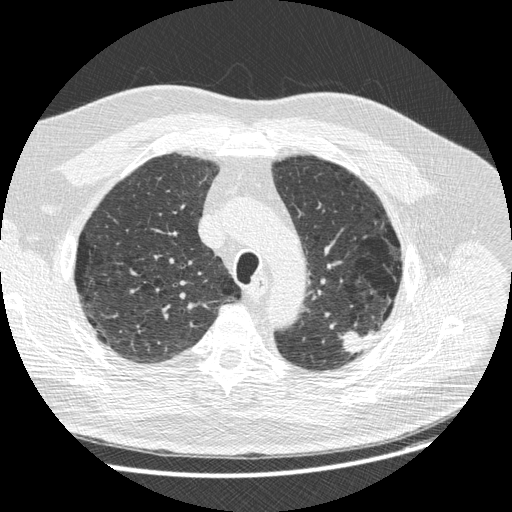
Low-dose screening chest CT, one axial slice; slice 202 of 258 in the series (ordered by position); reconstruction kernel STANDARD; lung window (W 1500 / L -600 HU); 512 × 512 image matrix.
Annotated regions visible in this slice (manually delineated by an expert):
- lesion 1 (tumor, upper lobe of left lung): bounding box [x1, y1, x2, y2] px = [341, 331, 377, 354]